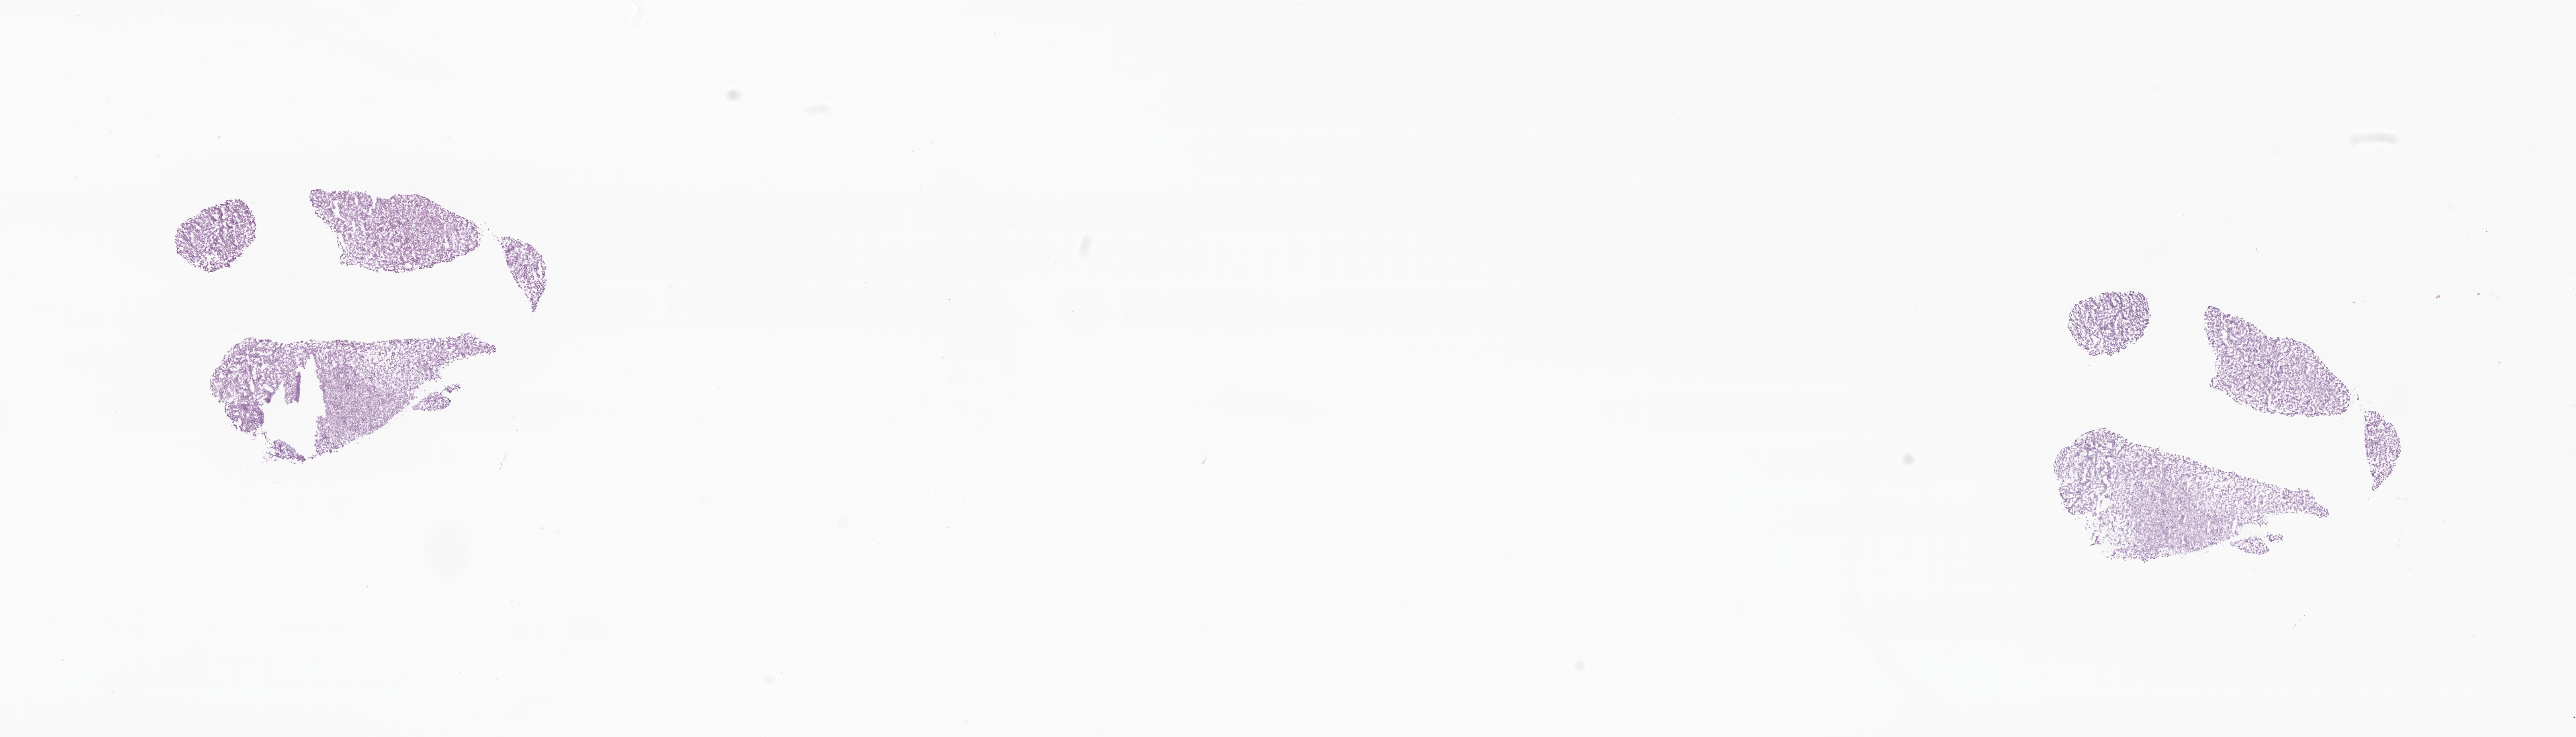
Digitized hematoxylin and eosin (H&E)-stained section — a low-resolution overview of the entire scanned area, about 27.0 x 7.7 mm. Cryosection. Specimen: metastatic tumor tissue. Female patient; age at initial diagnosis 50 years. Pathologist review of this section (percent, as recorded): tumor cells 95%, tumor nuclei 95%, stromal cells 5%, necrosis 0%, normal cells 0%. Infiltration values recorded for this section: lymphocyte infiltration 0%, monocyte infiltration 0%, neutrophil infiltration 0%.
Section: bottom of the tissue portion. Patient diagnosis (primary): Adenocarcinoma, metastatic, NOS.